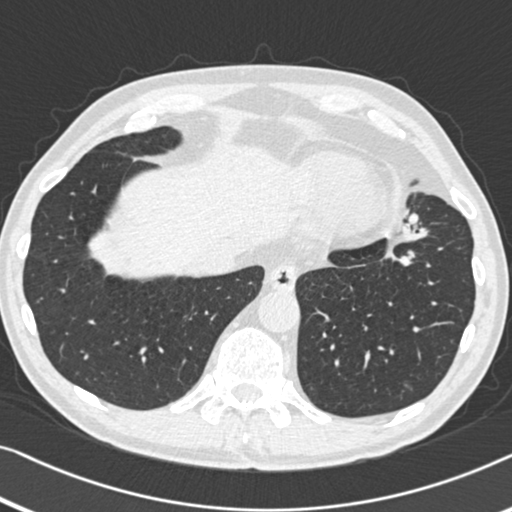
Low-dose screening chest CT, one axial slice. Reconstruction kernel B30f. 120 kVp. Lung window (W 1500 / L -600 HU). 1 mm slice thickness. 512 × 512 image matrix, field of view 332 × 332 mm.
Annotated regions visible in this slice (manually delineated by an expert):
- lesion 1 (tumor, upper lobe of left lung): bounding box (x1, y1, x2, y2) in pixels: (407, 213, 418, 225)